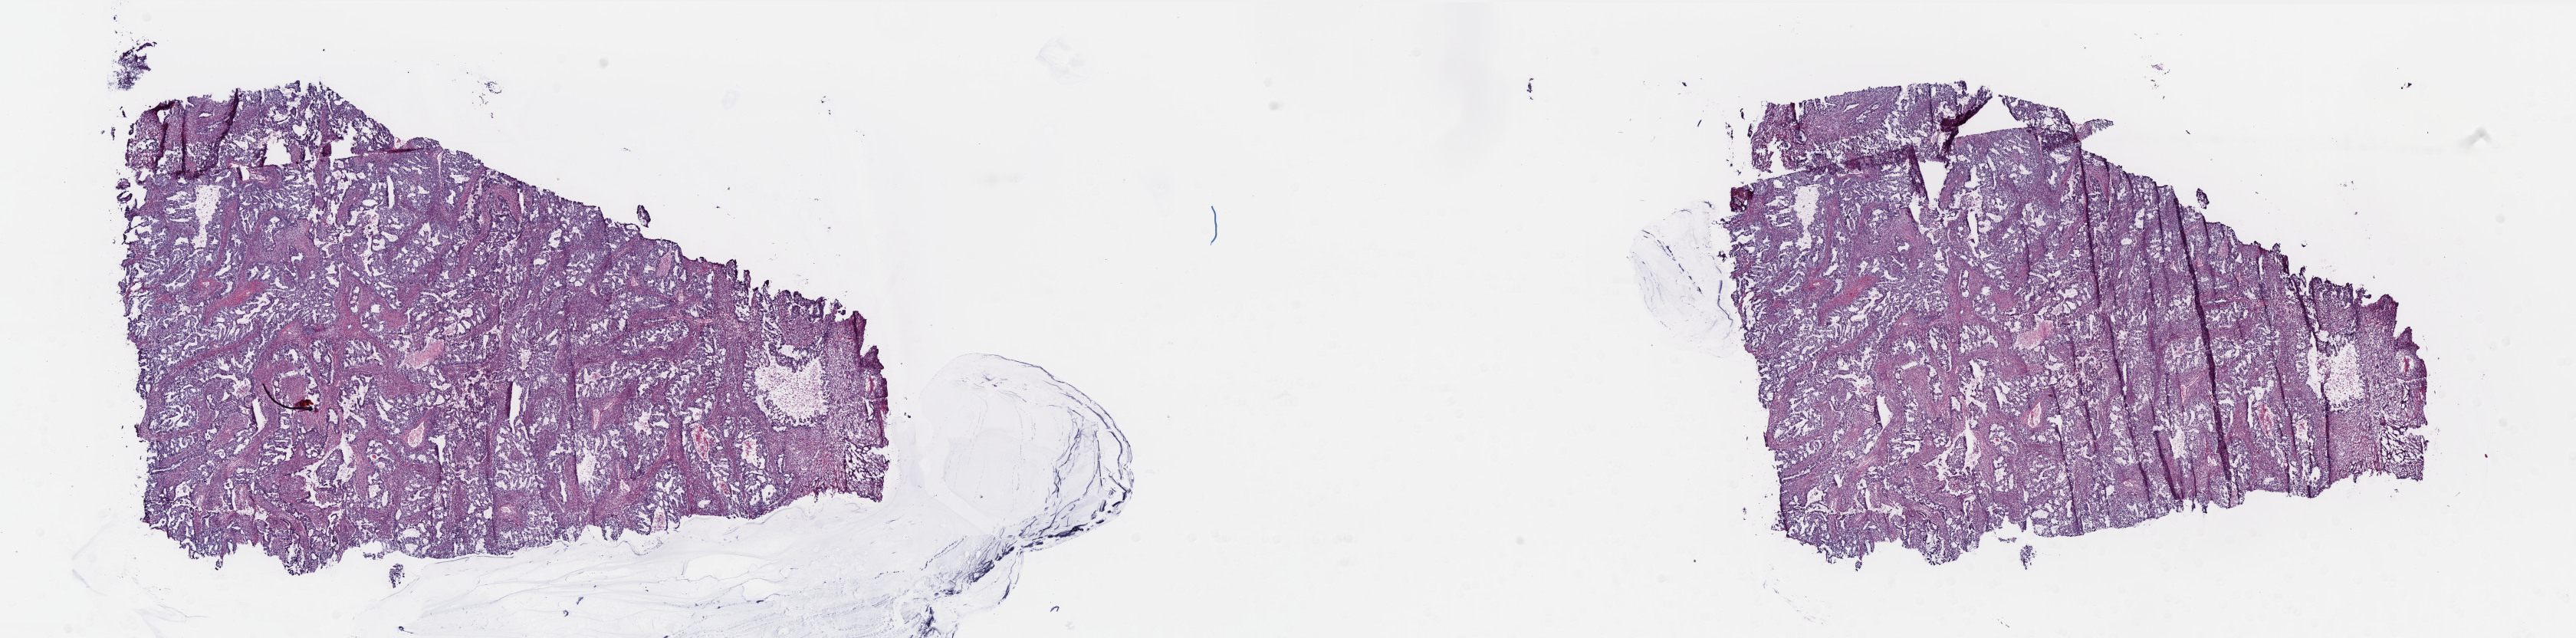
Digitized Hematoxylin and eosin (H&E) stained tissue section (whole slide), shown as a low-resolution overview of the whole scanned area (about 26.9 x 6.7 mm, slide scanned at 40x); frozen section; uterus, primary tumour sample. Patient: female, age at initial diagnosis 60 years. Histologic grade: G2 (moderately differentiated). Pathologist review of this section (percent, as recorded): tumour cells 75%, tumour nuclei 75%, normal cells 0%, stromal cells 25%, necrosis 0%. Inflammatory infiltration, as recorded: lymphocyte infiltration 0%, monocyte infiltration 0%, neutrophil infiltration 0%.
• lymph nodes positive (case pathology): 2 of 8 examined
• FIGO stage: IIIC
• diagnosis: Endometrioid adenocarcinoma, NOS (endometrium)